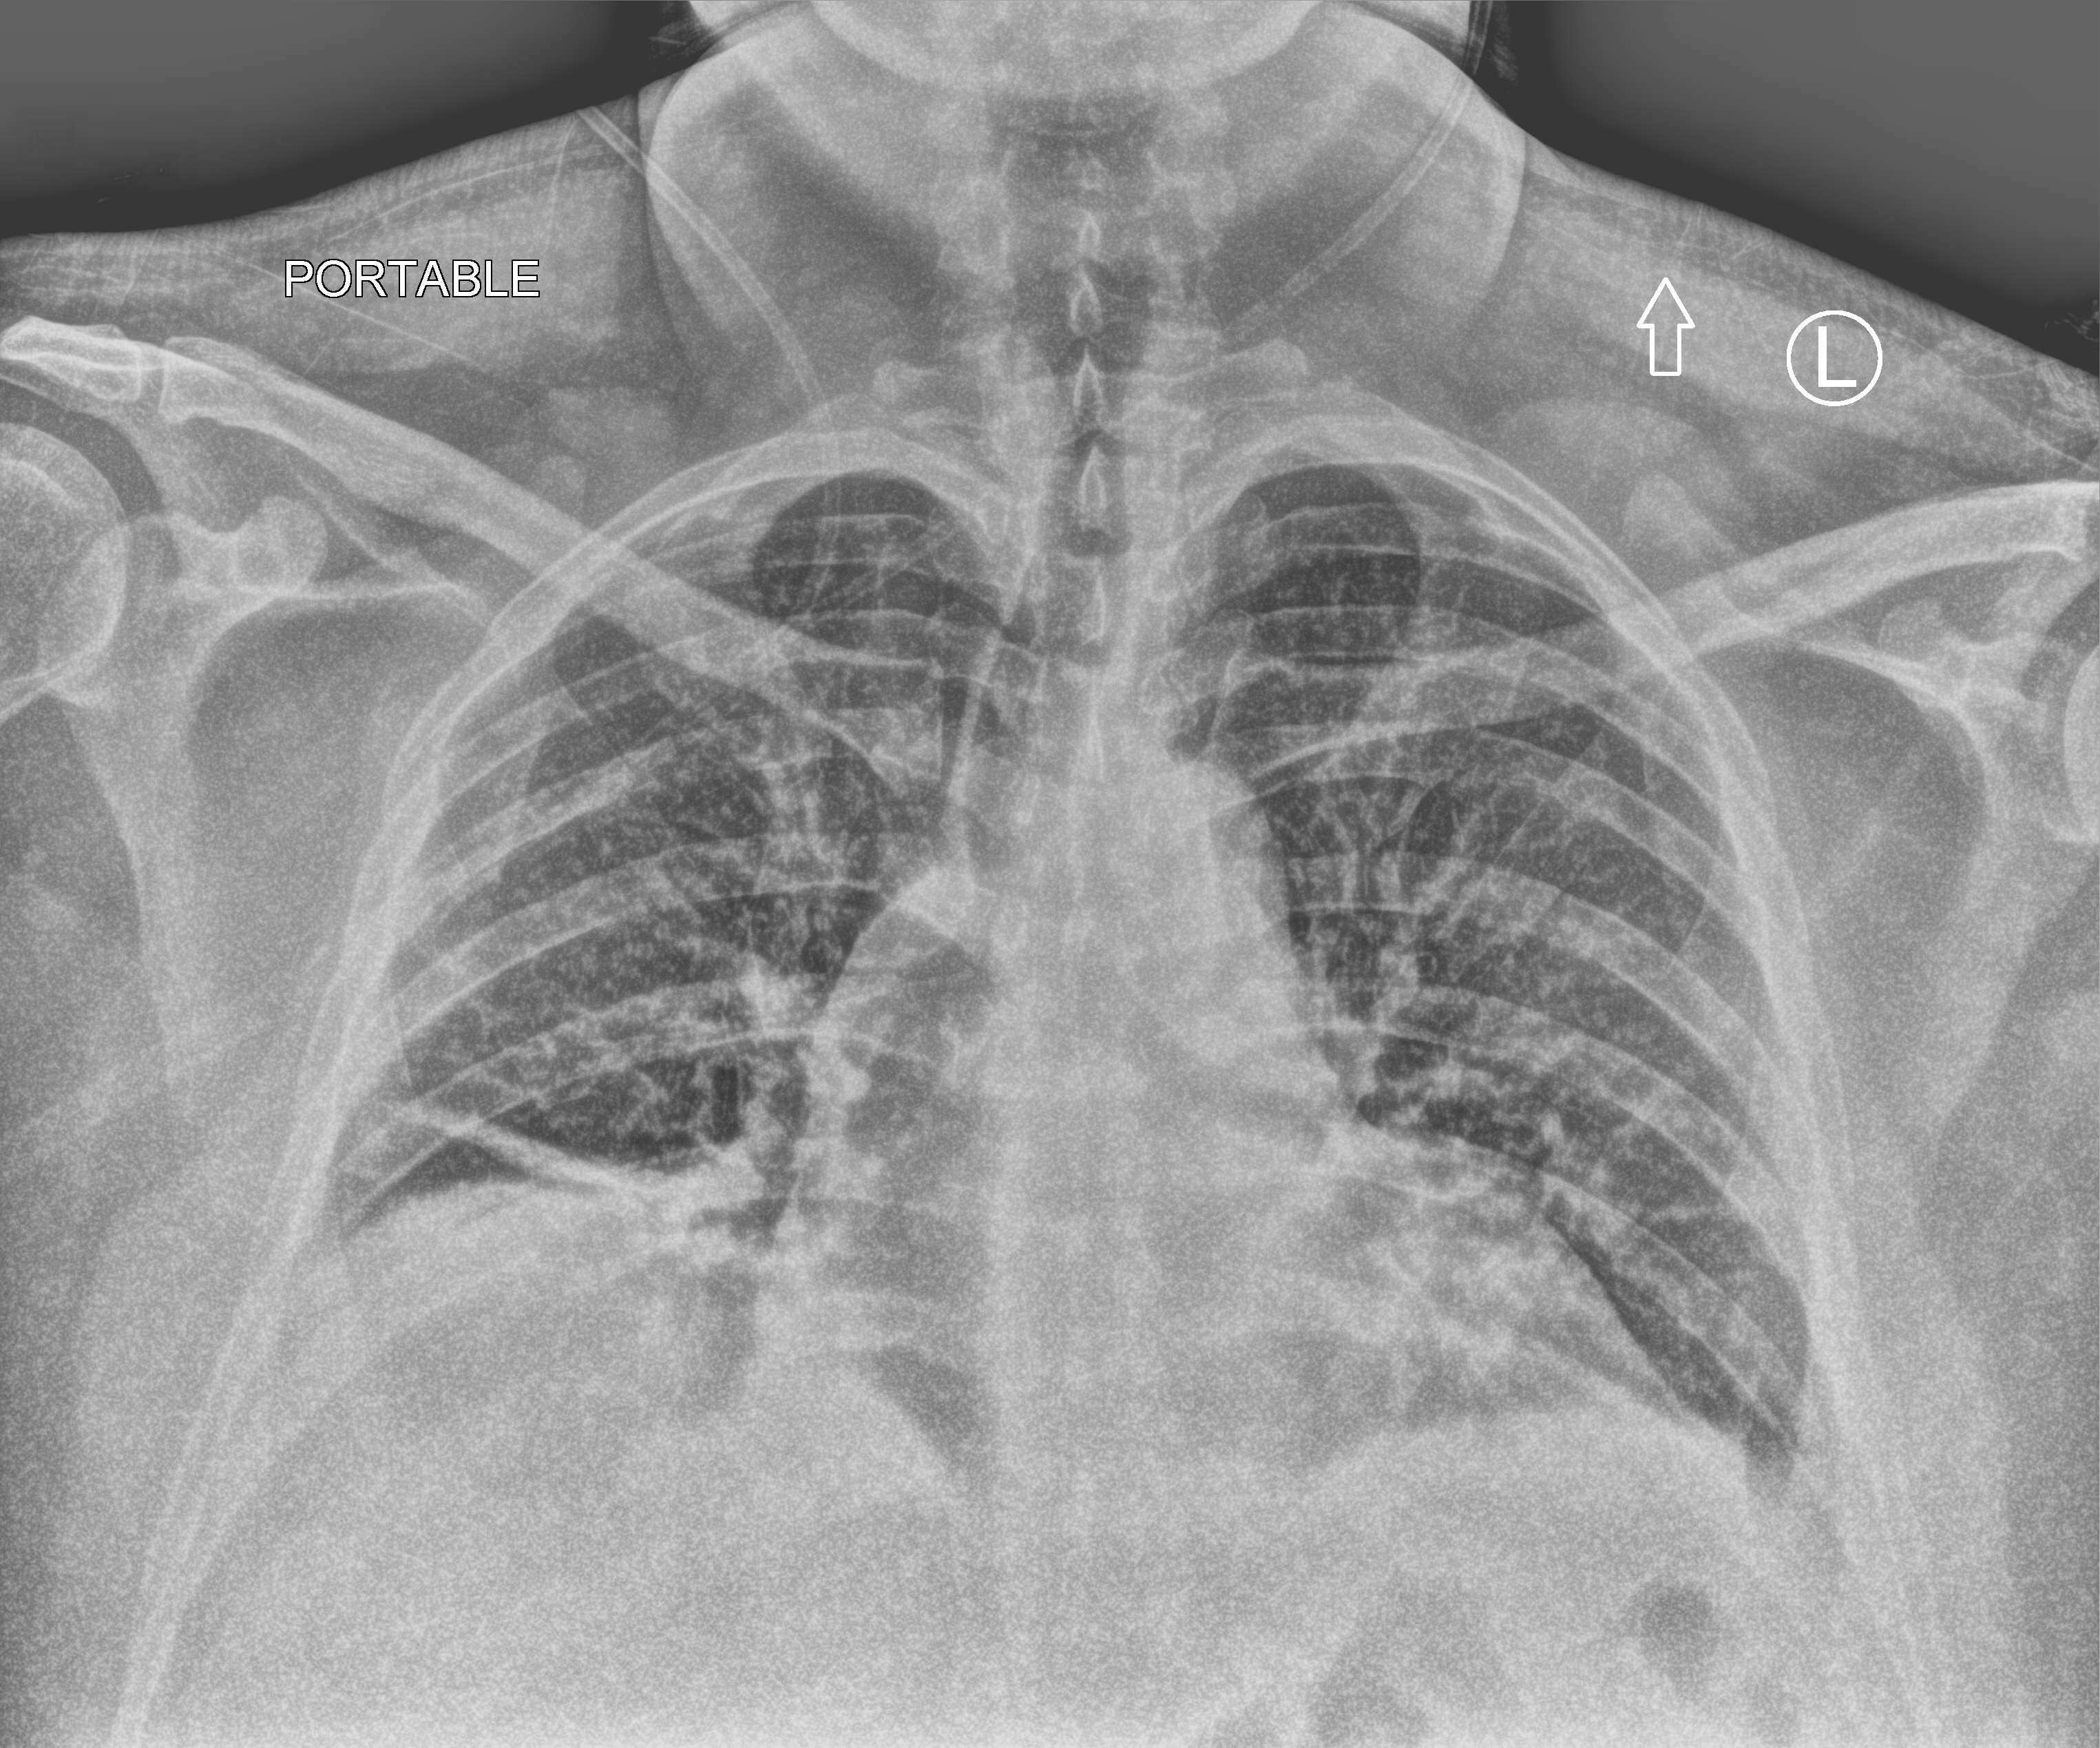
Bedside chest radiograph (computed radiography). Patient hospitalised with COVID-19, aged 18–59 years.
From the hospital-stay record, not from the radiograph (when in the stay this image was taken is not recorded):
- admitted to intensive care during this hospital stay: yes